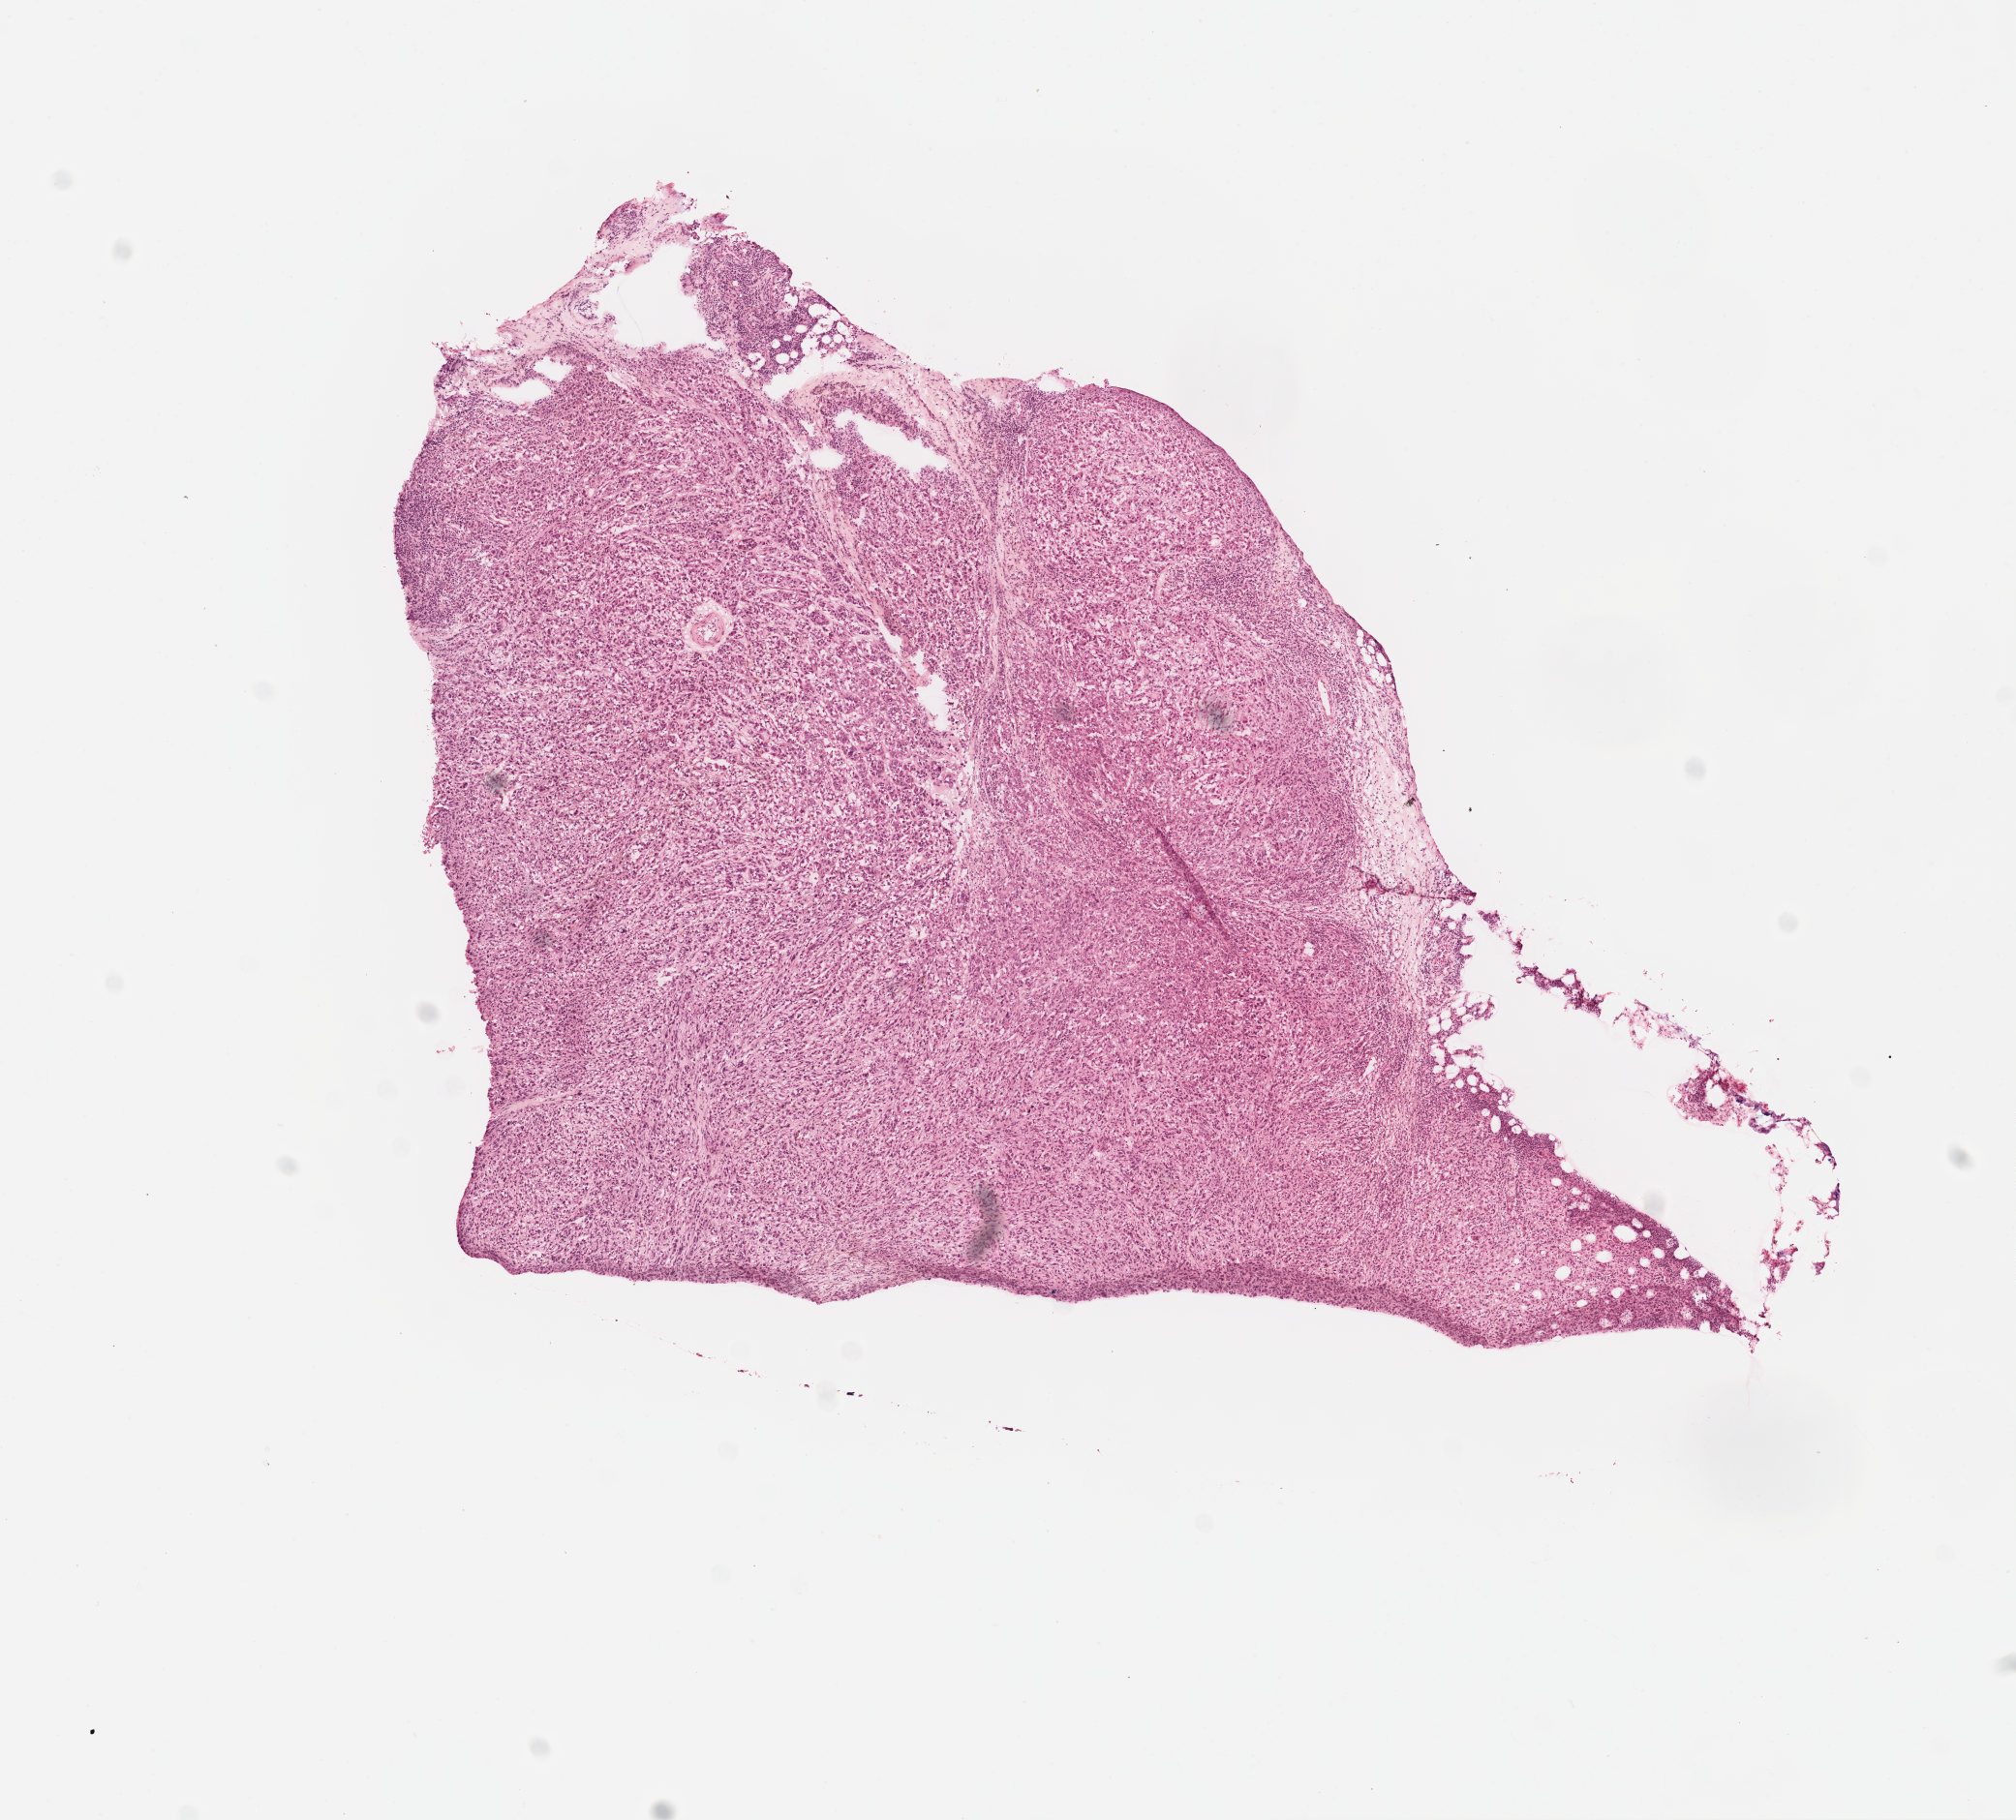
Digitized H&E tissue section (whole slide) — shown as a low-resolution overview of the whole scanned area (about 8.2 x 7.4 mm, from a 40x scan); FFPE section; metastatic tumour sample. Male patient; age at initial diagnosis 71 years.
- this section: metastatic tumour tissue
- patient diagnosis: Malignant melanoma, NOS